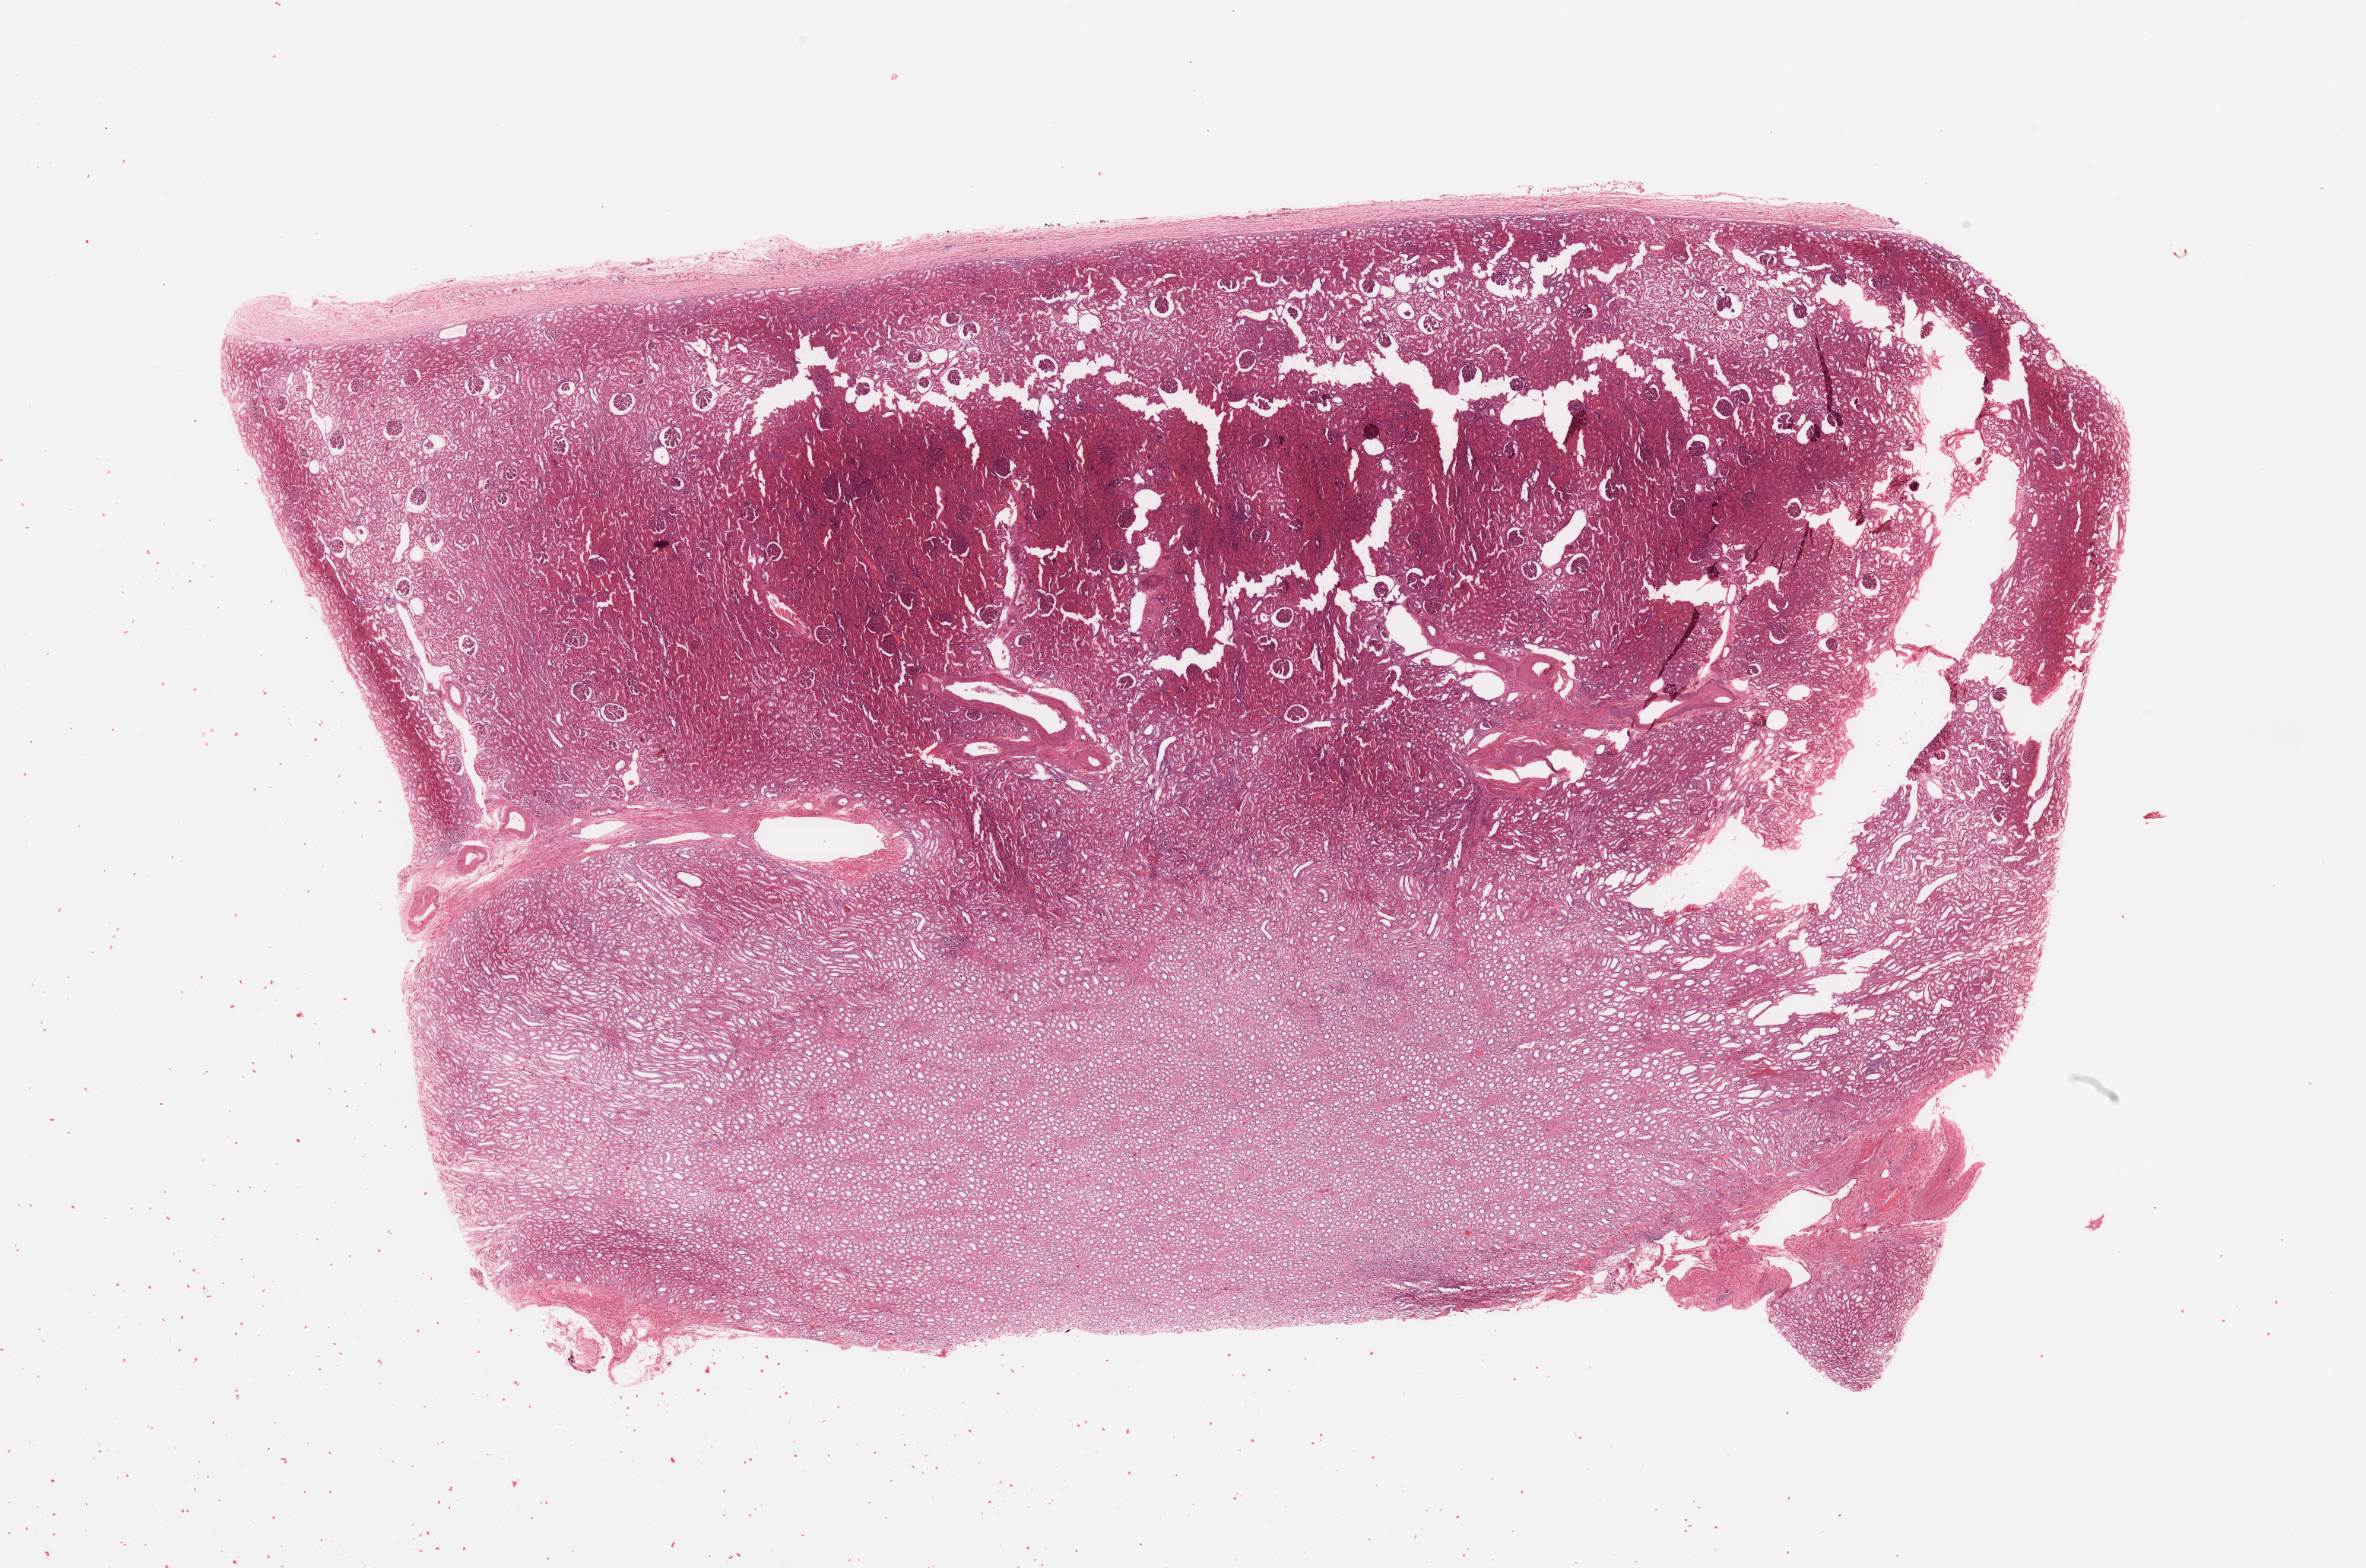
Whole-slide histology image, H&E — whole scanned area (about 24.6 x 16.3 mm, slide scanned at 20x) shown as a low-resolution overview; normal (non-tumour) tissue sample, sampled site: kidney. Patient: female, age 57 years.
* this section: normal (non-tumour) tissue from the same patient
* patient diagnosis: Renal cell carcinoma, NOS